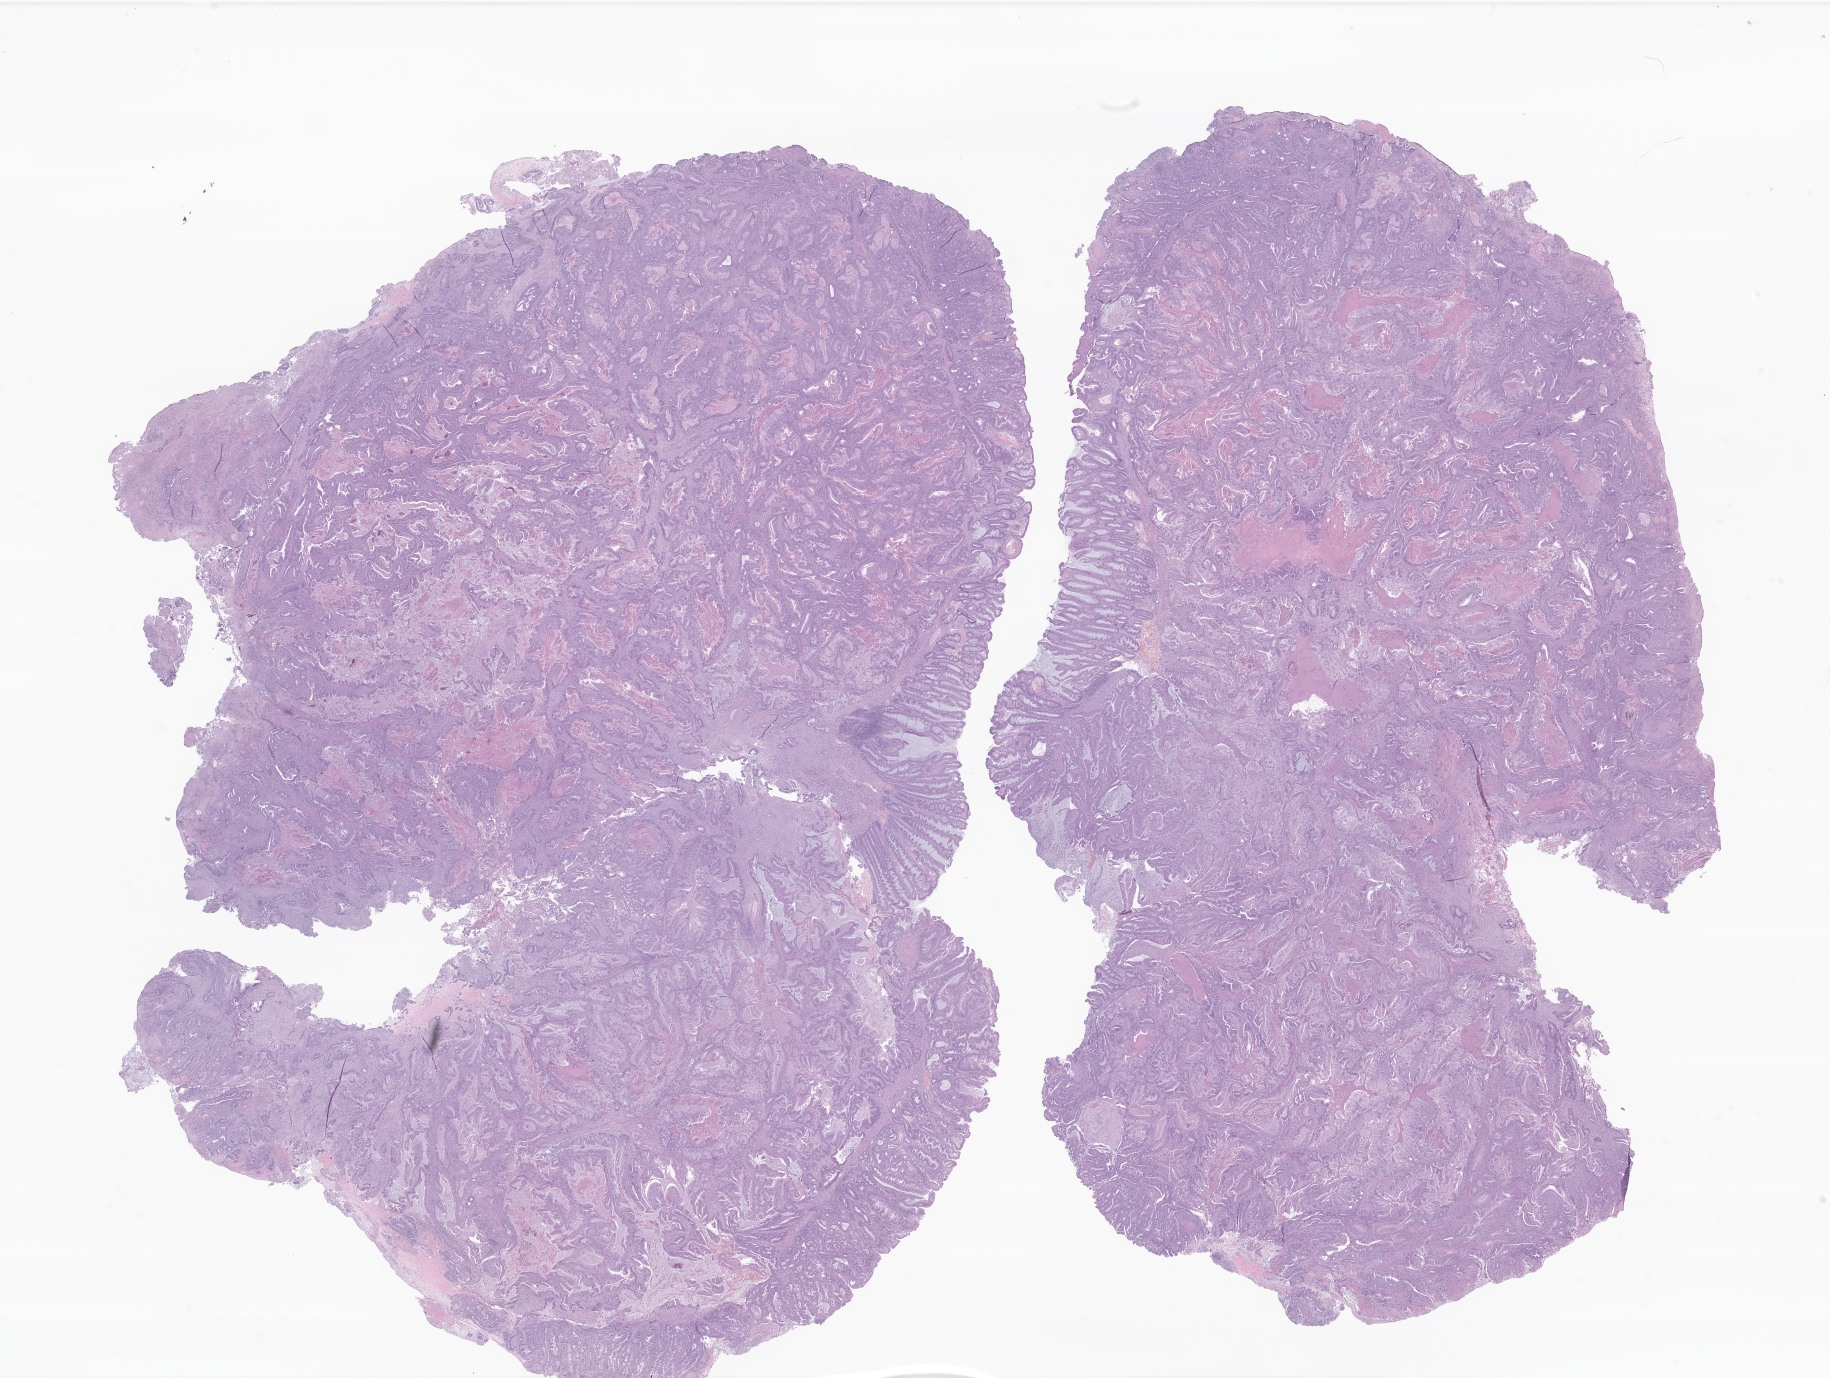
Haematoxylin and eosin whole-slide image of tumor tissue from the rectum, a low-resolution overview of the entire scanned area, about 30.9 x 23.2 mm; FFPE section. Patient male; age 181 months (15 years 1 month).
- diagnosis: Adenocarcinoma, NOS